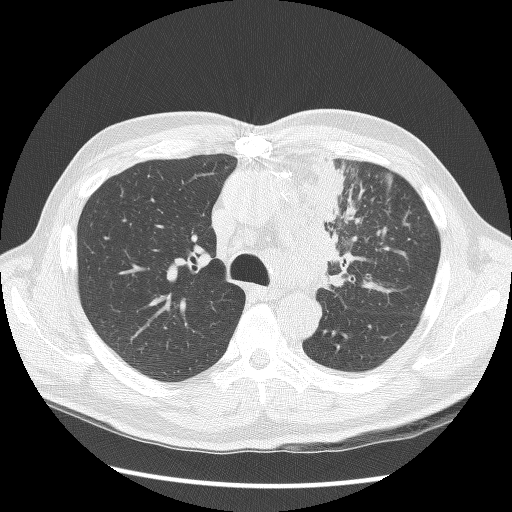
Low-dose screening chest CT, axial slice; second screening round (one year after baseline); lung window (W 1500 / L -600 HU); lung (sharp) reconstruction kernel (BONE); 512 × 512 image matrix. Male participant, aged 64 years at enrolment.
Expert reader's lesion annotation, bounding box <299,161,374,288> (left, top, right, bottom; pixels). Screening reader's record for this exam: no non-calcified nodule ≥4 mm recorded. Official screen result: positive, other. Lung cancer was diagnosed 24 days after this screen: small cell carcinoma, NOS, left upper lobe, stage IV (AJCC 6th edition), 100 mm at pathology.